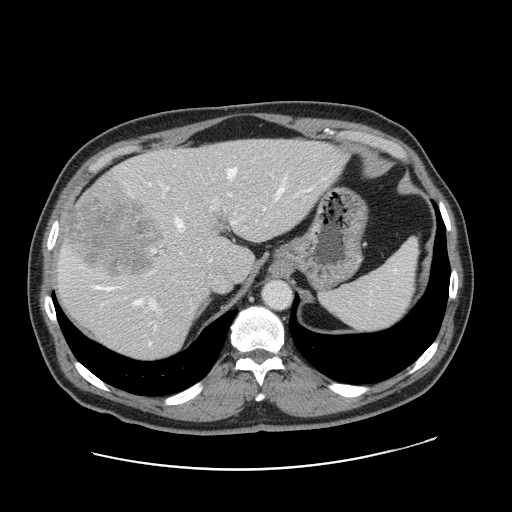
Contrast-enhanced abdominal CT, one axial slice; slice 120 of 178 in the series (ordered by position); intravenous contrast given; soft-tissue window (W 400 / L 40 HU); 2.5 mm slice thickness; 512 × 512 image matrix, field of view 403 × 403 mm. Male patient, age 63 years. Case-level facts recorded for this patient, not image findings: diagnosis: colorectal cancer liver metastases, imaged before liver resection; multiple liver metastases: yes; largest metastasis: 8 cm; disease in both lobes: yes.
Structures marked on this image (expert manual segmentation):
- hepatic veins: box from (x=93, y=168) to (x=284, y=304) px
- liver: (x=57, y=140)–(x=344, y=360)
- planned liver remnant (the part of the liver to remain after resection): (x=142, y=140)–(x=344, y=280)
- portal vein (with intrahepatic branches): (x=151, y=187)–(x=238, y=328)
- liver metastasis: (x=65, y=195)–(x=162, y=277)